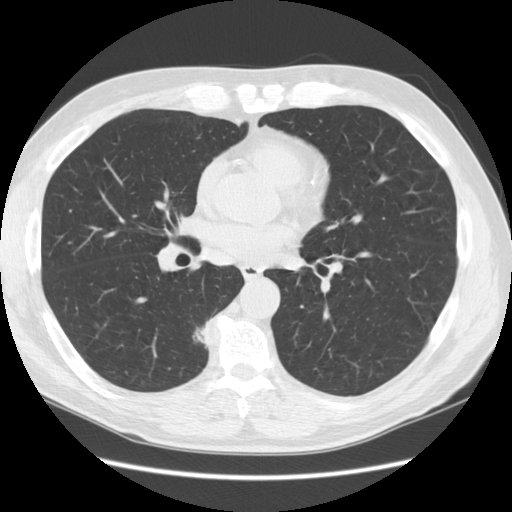
Low-dose screening chest CT, one axial slice. Position 65 of 133 along the scan axis. Lung window (W 1500 / L -600 HU). 512 × 512 image matrix.
Structures marked on this image (expert manual segmentation):
- lesion 1 (tumor, lower lobe of right lung): bounding box (x1, y1, x2, y2) in pixels: (193, 318, 213, 344)